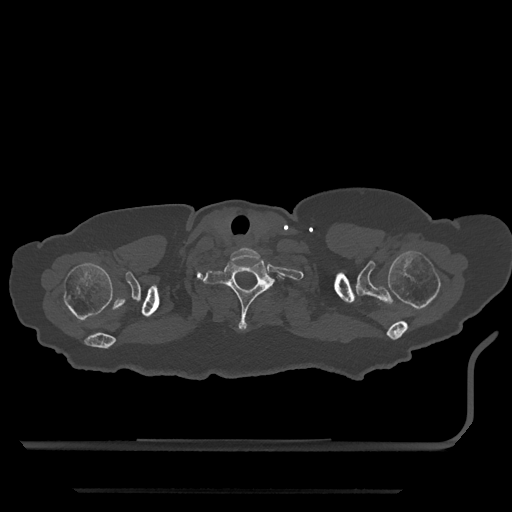
CT including the spine, one axial slice; 120 kVp; bone window (W 1800 / L 400 HU); 0.5 mm slice thickness; 512 × 512 image matrix. Female patient, age 51 years. From the clinical record (not read from this slice): primary cancer: neuro; vertebrae with lytic lesions (as recorded): T8.
Annotated regions visible in this slice (semi-automatically segmented with operator editing):
- T1 vertebra: bounding box (x1, y1, x2, y2) in pixels: (204, 260, 283, 331)